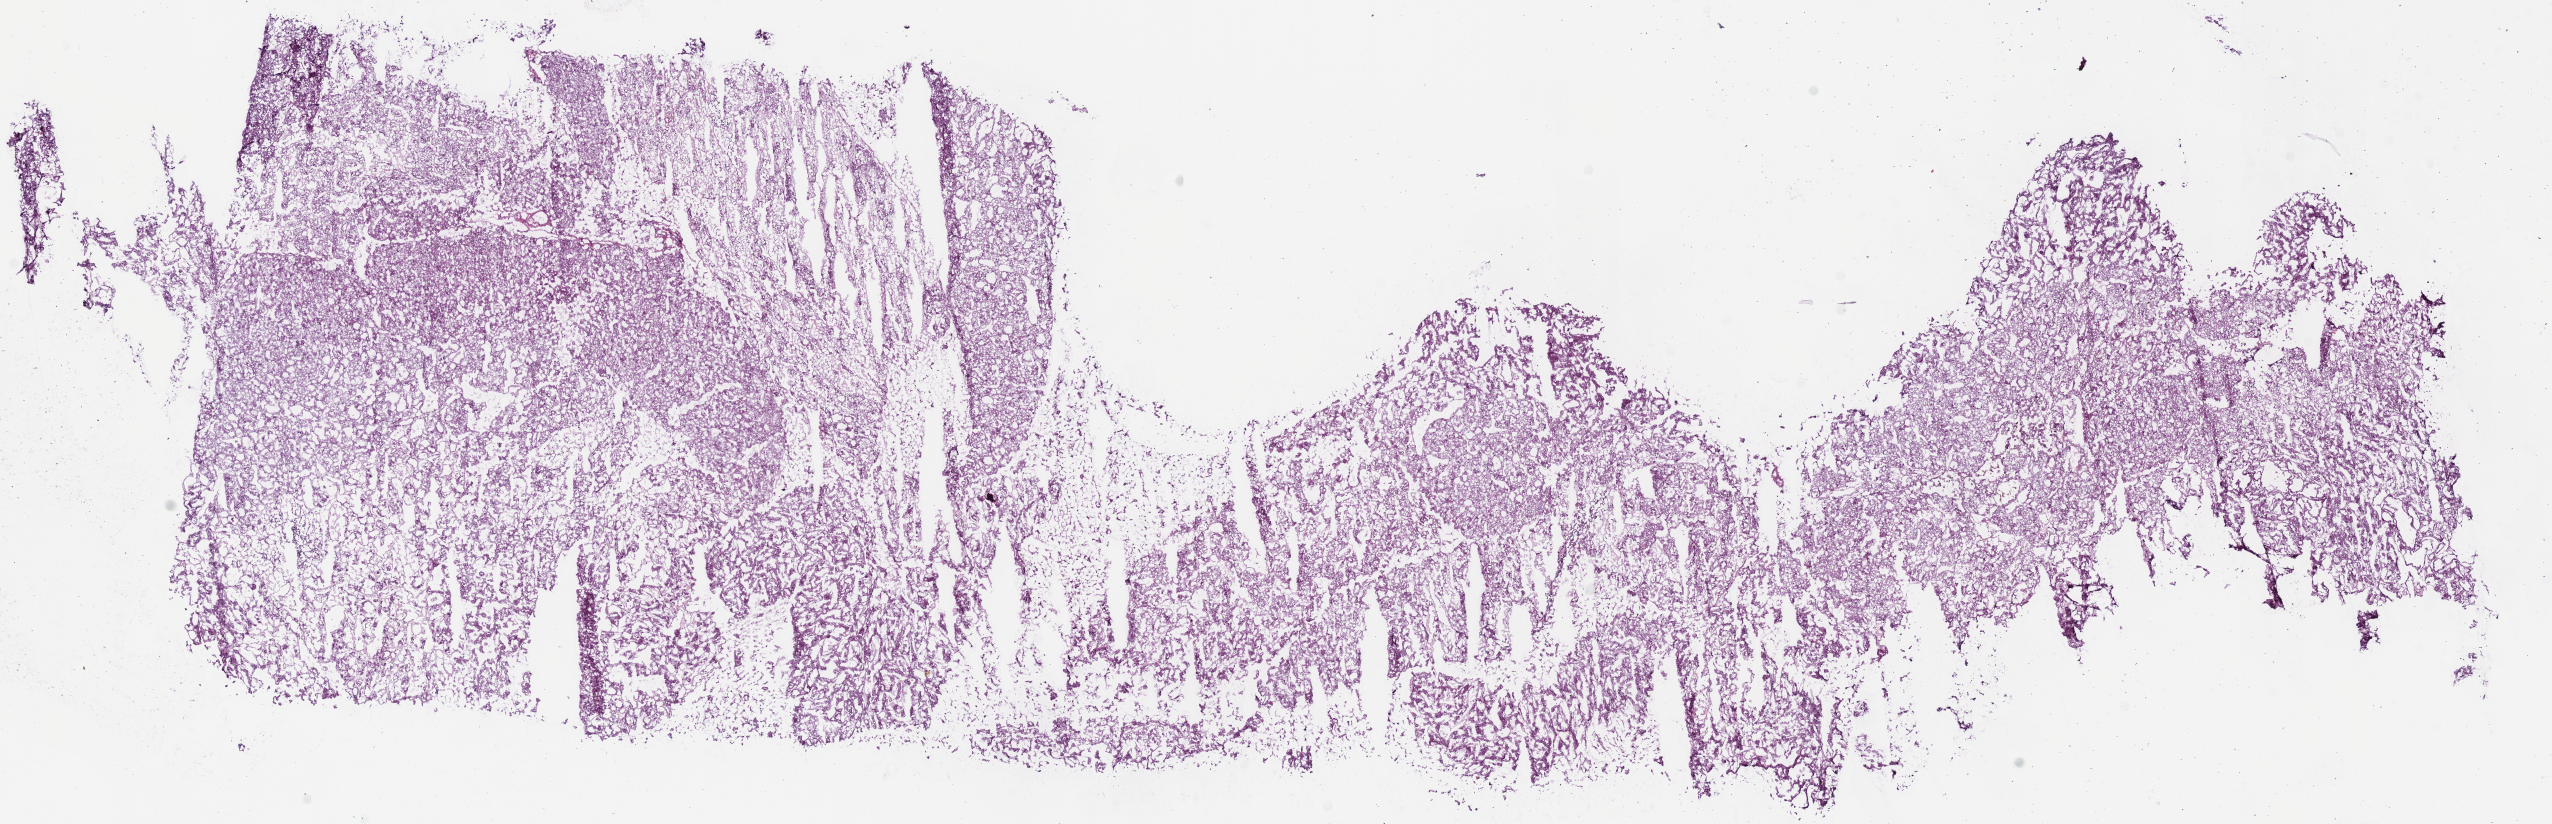
H&E-stained whole-slide image, a low-resolution overview of the entire scanned area, about 20.1 x 6.5 mm (acquisition: 40x scan). Frozen section from the bottom of the tissue portion. Primary tumour sample from the kidney. Female patient; age at initial diagnosis 74 years. Slide review estimates, as recorded: tumour cells 90%, tumour nuclei 90%.
Histologic diagnosis: Renal cell carcinoma, chromophobe type.